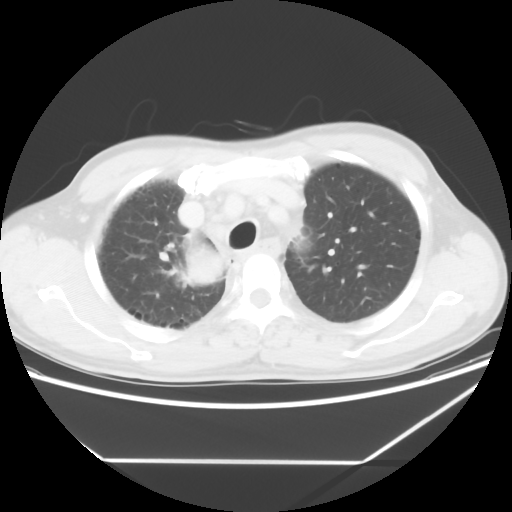
Chest CT, one axial slice. Slice 47 of 60 in the series (ordered by position). Reconstruction kernel STANDARD. 120 kVp. Lung window (W 1500 / L -600 HU). 5 mm slice thickness. 512 × 512 image matrix, field of view 367 × 367 mm. Male patient, age 58 years. Case-level facts recorded for this patient, not image findings: clinical TNM (as recorded): T2 N2 M0.
Structures marked on this image (rectangle marked by the reading radiologist):
- lung tumour (recorded histology: squamous cell carcinoma): bounding box <174,236,237,294> (left, top, right, bottom; pixels)